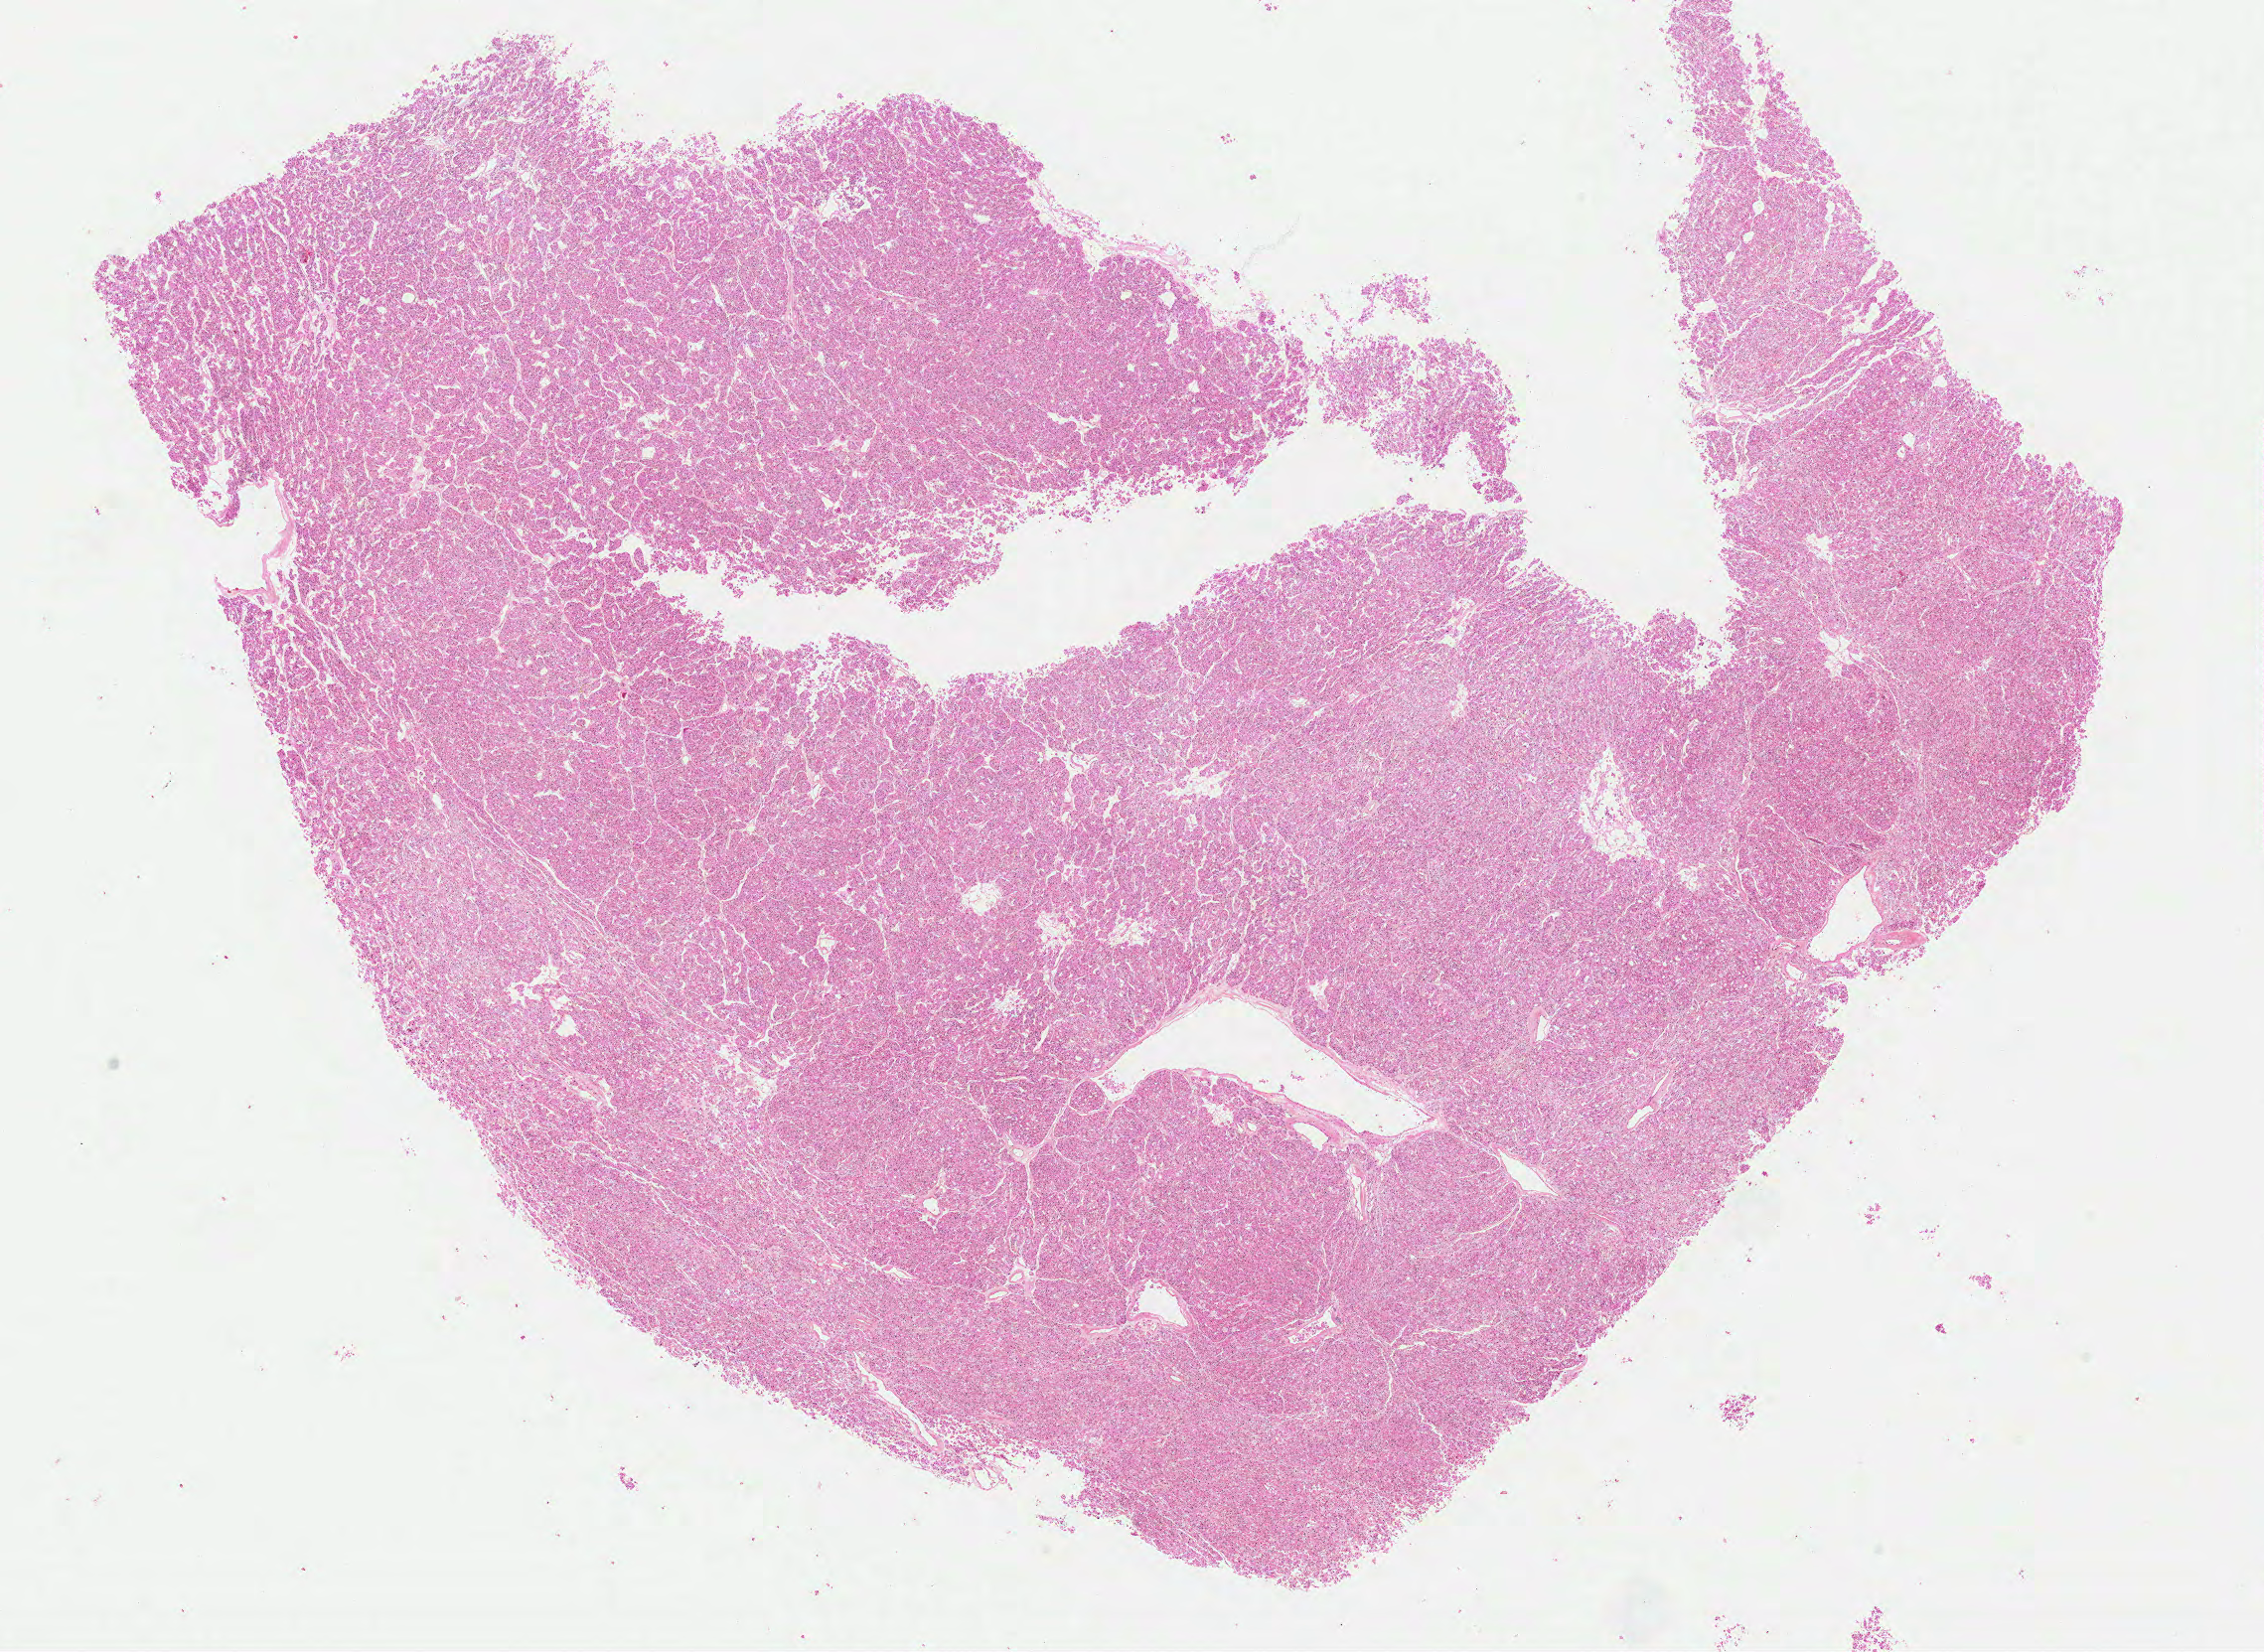
Digitized H&E tissue section (whole slide), a low-resolution overview of the entire scanned area, about 18.0 x 13.2 mm; formalin-fixed paraffin-embedded (FFPE) diagnostic section; kidney, primary tumour sample. Male patient; age at initial diagnosis 83 years. Histologic grade: G2 (moderately differentiated).
* diagnosis: Clear cell adenocarcinoma, NOS
* AJCC pathologic stage: II